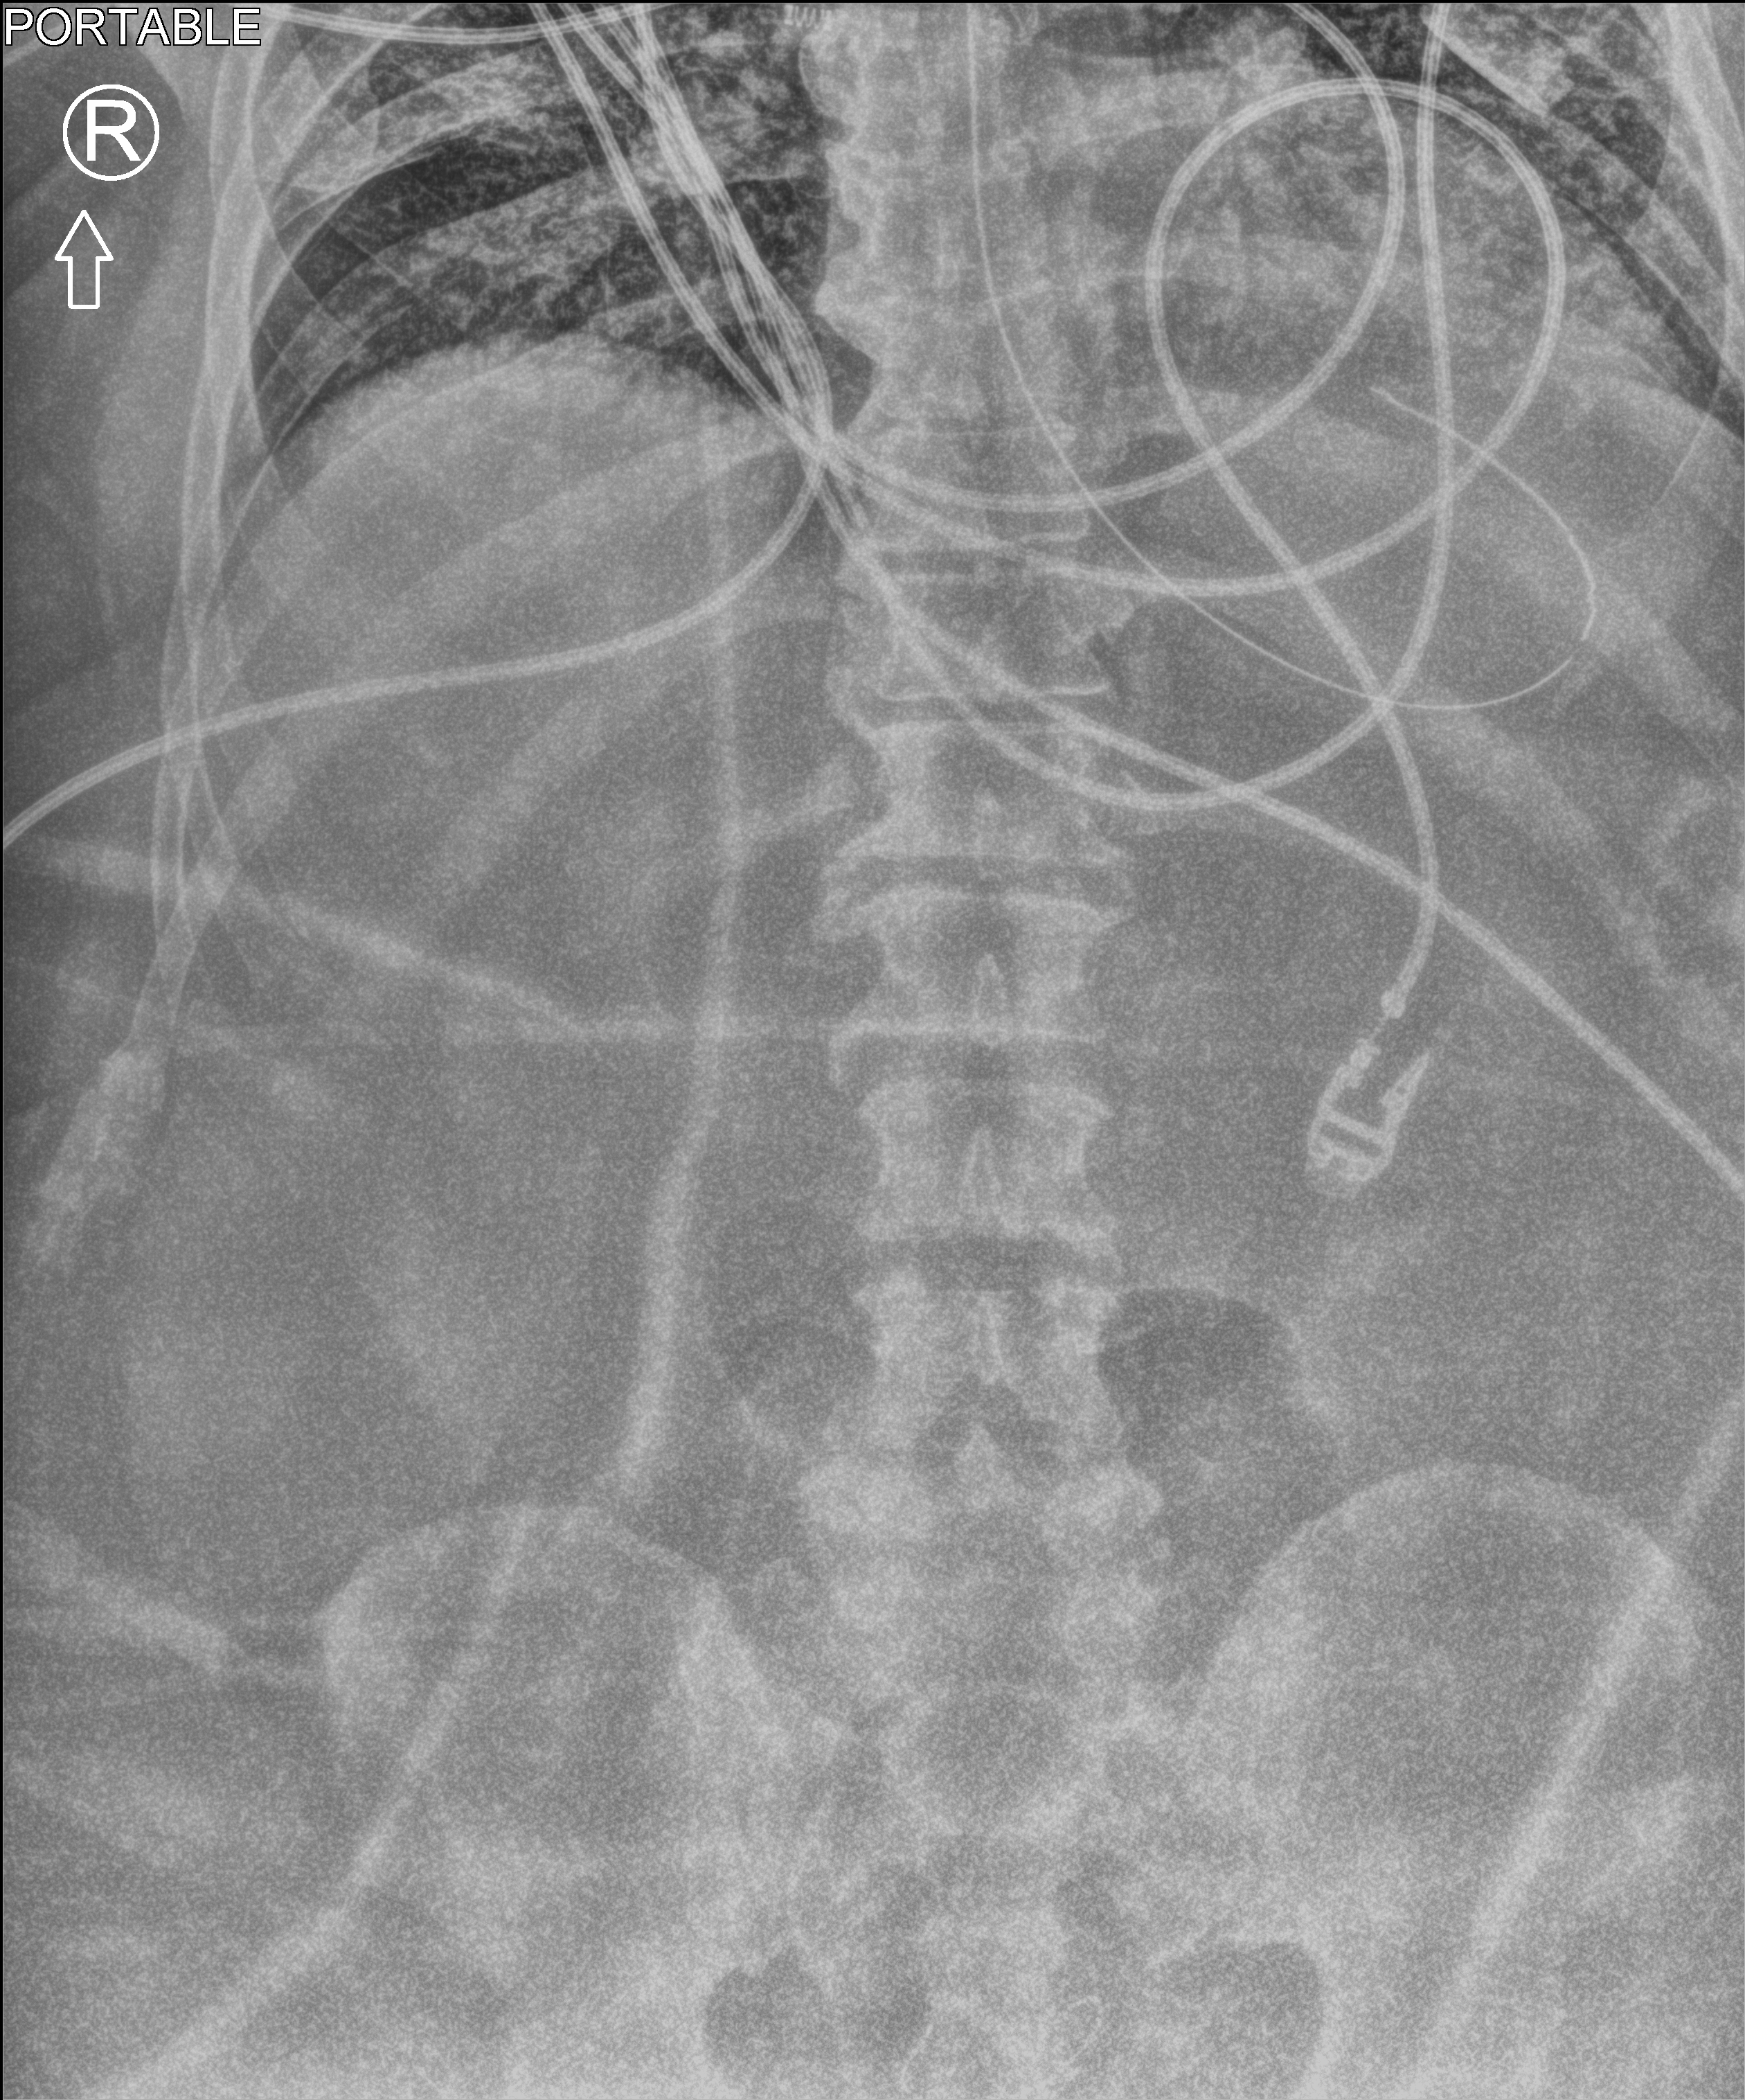
Portable abdomen radiograph, anteroposterior (AP) projection. Patient hospitalised with COVID-19, aged 18–59 years.
Hospital-stay facts (about this admission, not read from this image; timing relative to this image not recorded): length of hospital stay: 28 days; admitted to intensive care during this hospital stay: yes.